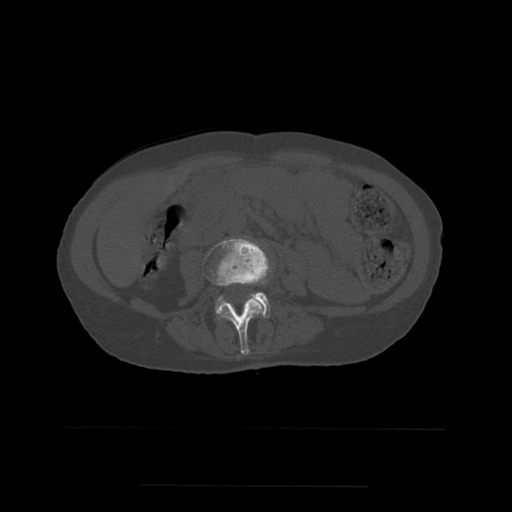
CT including the spine, one axial slice; position 181 of 544 along the scan axis; bone window (W 1800 / L 400 HU); 1.25 mm slice thickness; 512 × 512 image matrix, field of view 350 × 350 mm. Patient age 58 years. From the clinical record (not read from this slice): primary cancer: lung.
Annotated regions visible in this slice (semi-automatic segmentation, software-assisted and operator-edited):
- L3 vertebra: bounding box (x1, y1, x2, y2) in pixels: (202, 238, 272, 355)
- L4 vertebra: (216, 281, 271, 318)